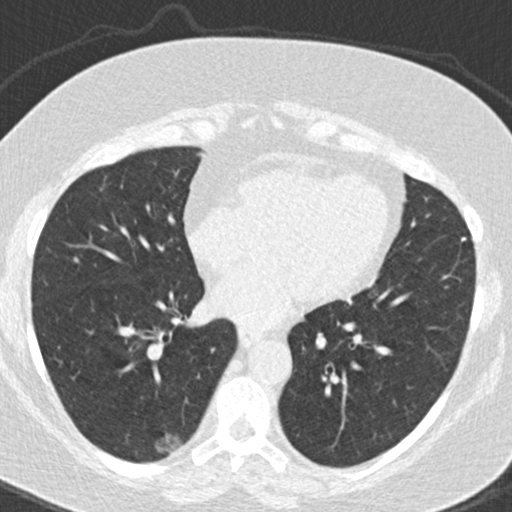
Chest CT (low-dose screening protocol), one axial image, baseline screening round, lung window (W 1500 / L -600 HU), slice 107 of 177 in the series, 512 × 512 image matrix. Female participant, aged 63 years at enrolment.
Lesion marked by an expert reader, bounding box <147,423,187,461> (left, top, right, bottom; pixels). Screening reader's record for this exam (one nodule recorded; not confirmed to be the boxed lesion): non-calcified nodule or mass ≥4 mm, right lower lobe, 16 × 10 mm, poorly defined margins, ground glass attenuation. Official screen result: positive, change unspecified: nodule(s) >= 4 mm or enlarging nodule(s), mass(es), or other non-specific abnormalities suspicious for lung cancer. Later outcome: lung cancer diagnosed 246 days after this screen — bronchiolo-alveolar adenocarcinoma, NOS, right lower lobe, well differentiated (G1), stage IA (AJCC 6th edition), 12 mm at pathology.